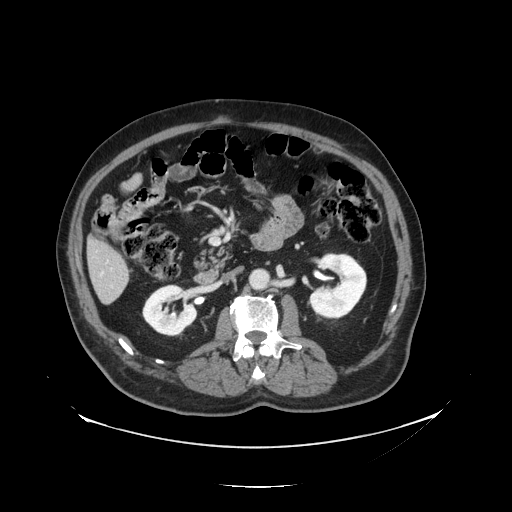
Contrast-enhanced abdominal CT, one axial slice; slice 46 of 138 in the series (ordered by position); intravenous contrast given; soft-tissue window (W 400 / L 40 HU); 2.5 mm slice thickness; 512 × 512 image matrix, field of view 497 × 497 mm. Male patient, age 77 years. Case-level facts recorded for this patient, not image findings: diagnosis: colorectal cancer liver metastases, imaged before liver resection.
Outlined on this slice (outlined manually by an expert reader):
- liver: bounding box [x1, y1, x2, y2] px = [89, 240, 130, 304]
- planned liver remnant (the part of the liver to remain after resection): [89, 240, 127, 278]